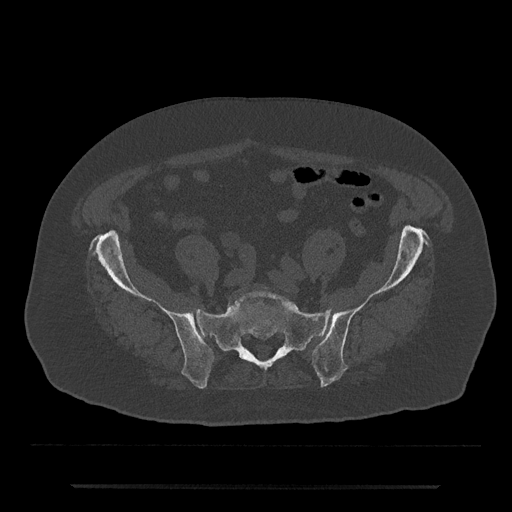
CT including the spine, one axial slice; position 235 of 797 along the scan axis; bone window (W 1800 / L 400 HU); 512 × 512 image matrix, field of view 434 × 434 mm. Male patient, age 80 years. Case-level facts recorded for this patient, not image findings: primary cancer: prostate; vertebrae with lytic lesions (as recorded): L1, T11.
Structures marked on this image (semi-automatically segmented with operator editing):
- L5 vertebra: bounding box (x1, y1, x2, y2) in pixels: (235, 291, 296, 307)